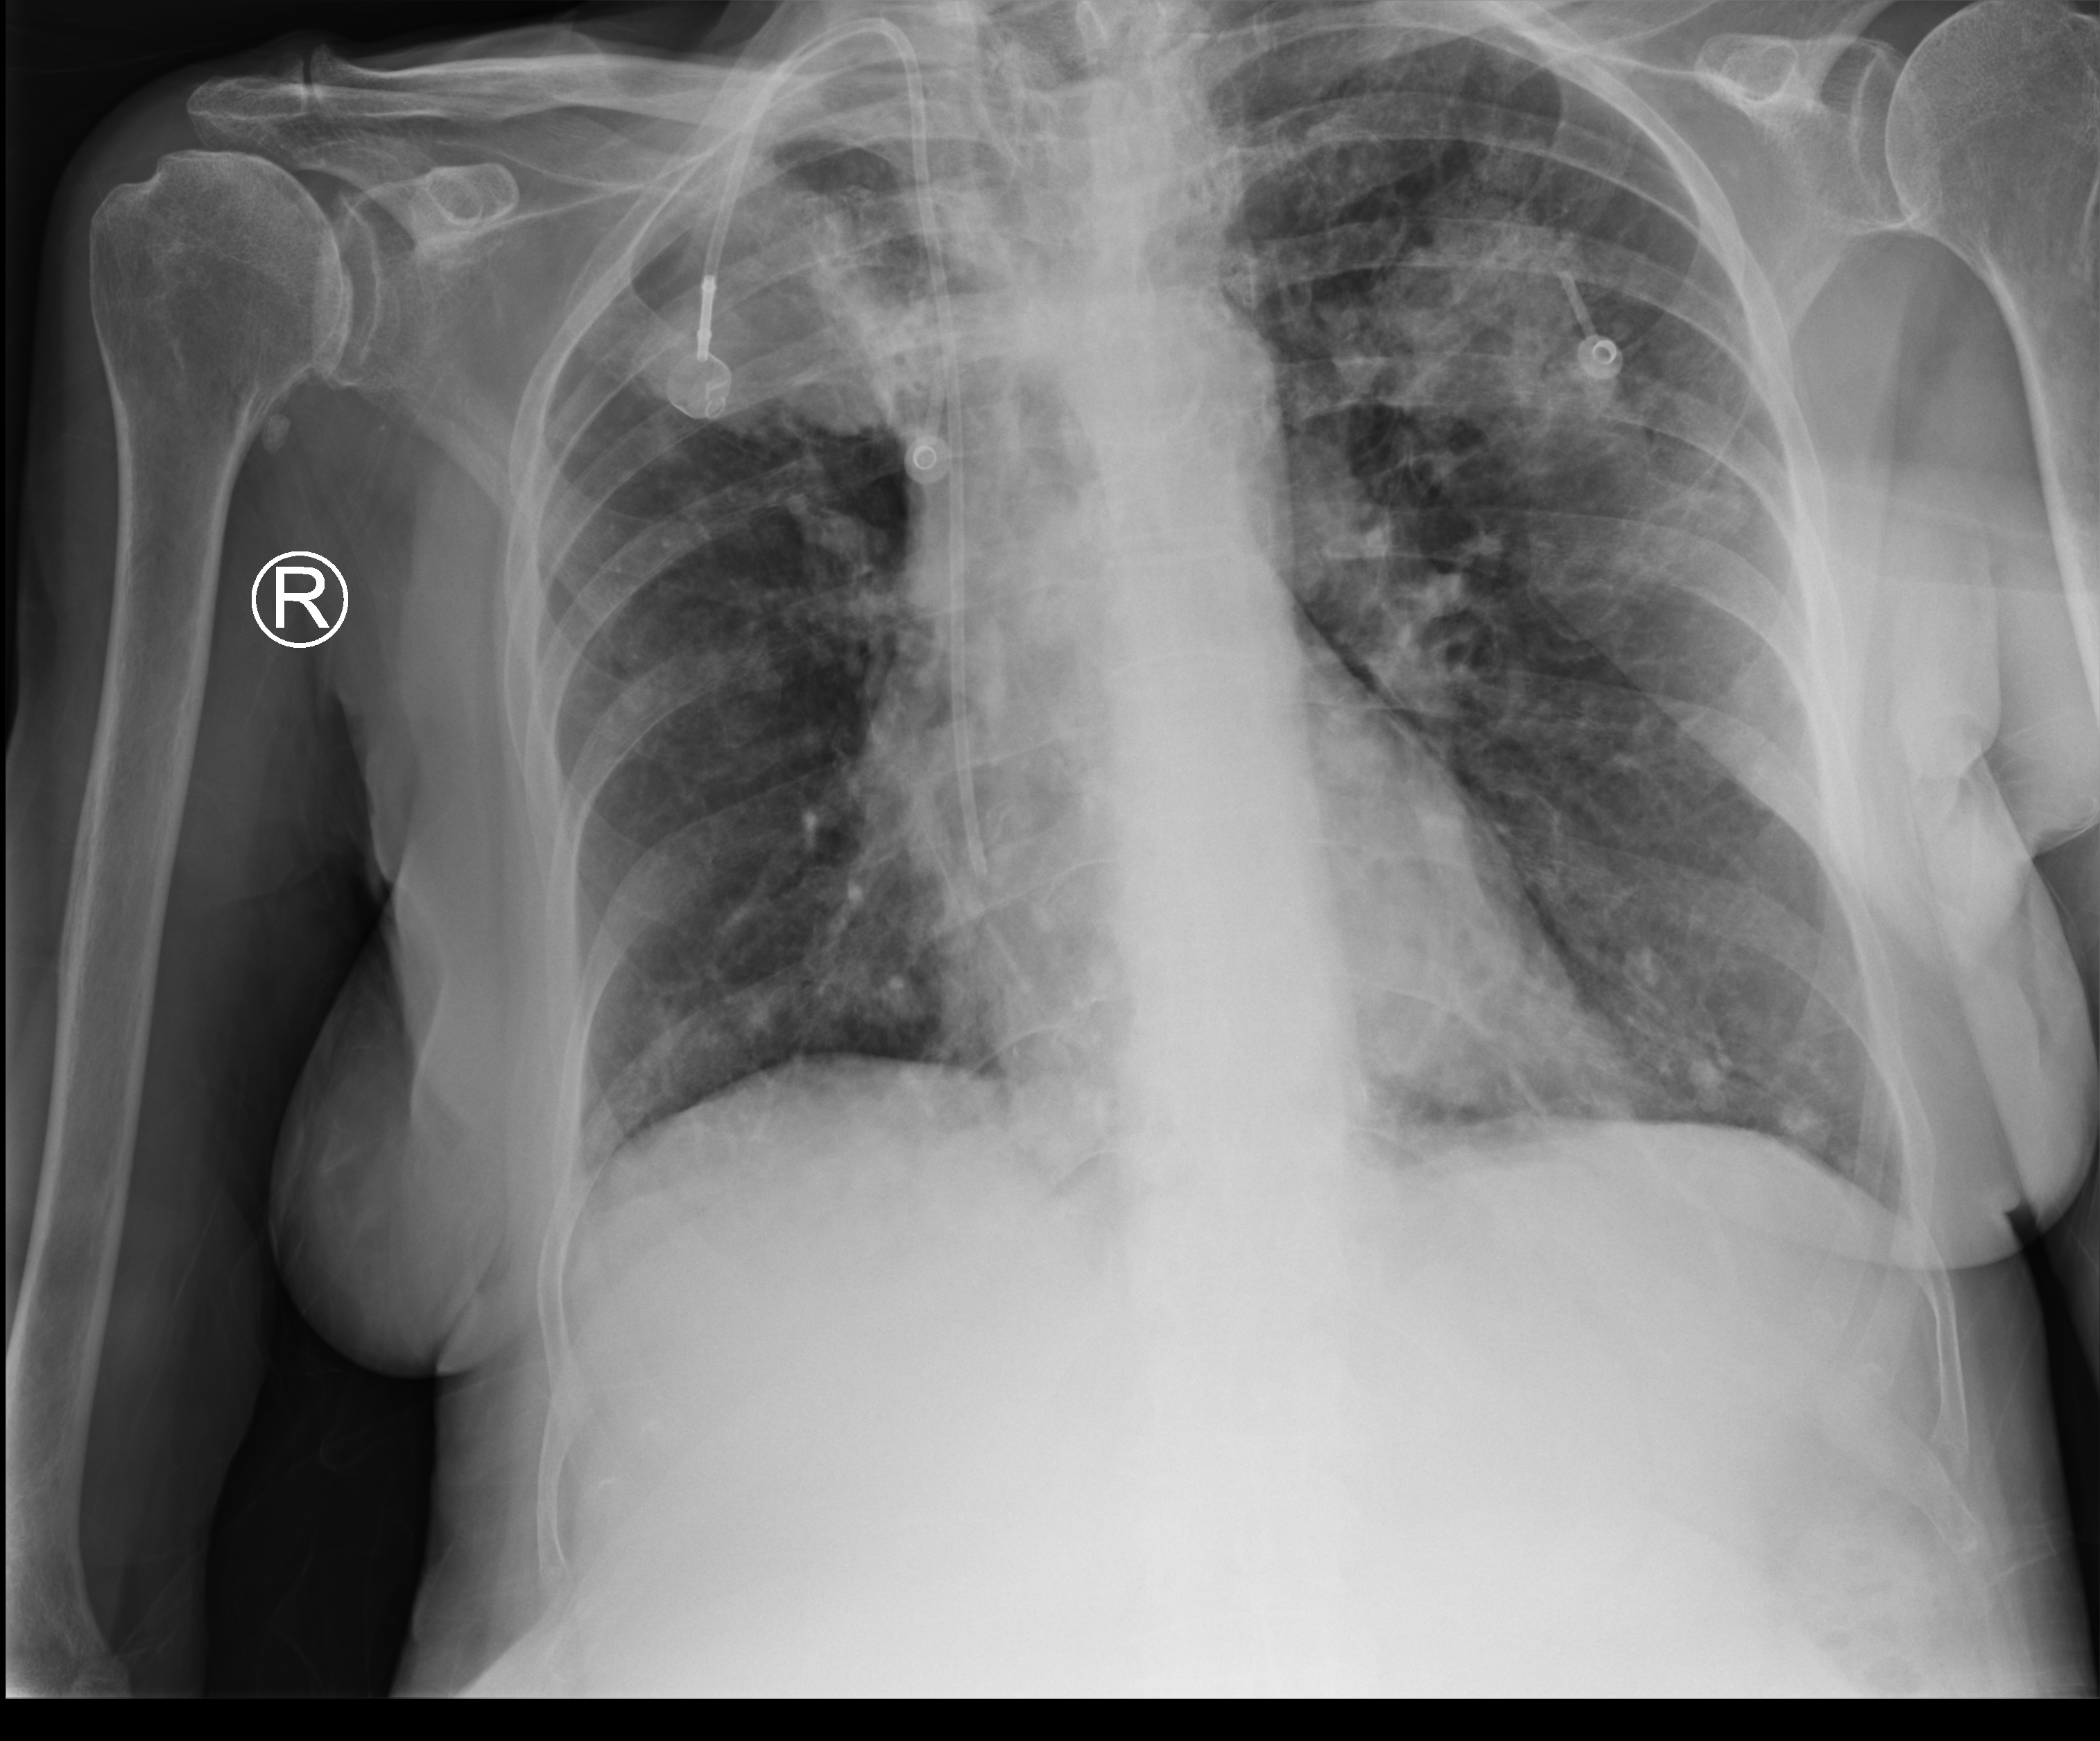
Chest X-ray (portable). Female patient hospitalised with COVID-19, age 60–74 years.
Admission-level facts for this patient (not findings on this image; timing relative to this image not recorded): admitted to intensive care during this hospital stay: no.